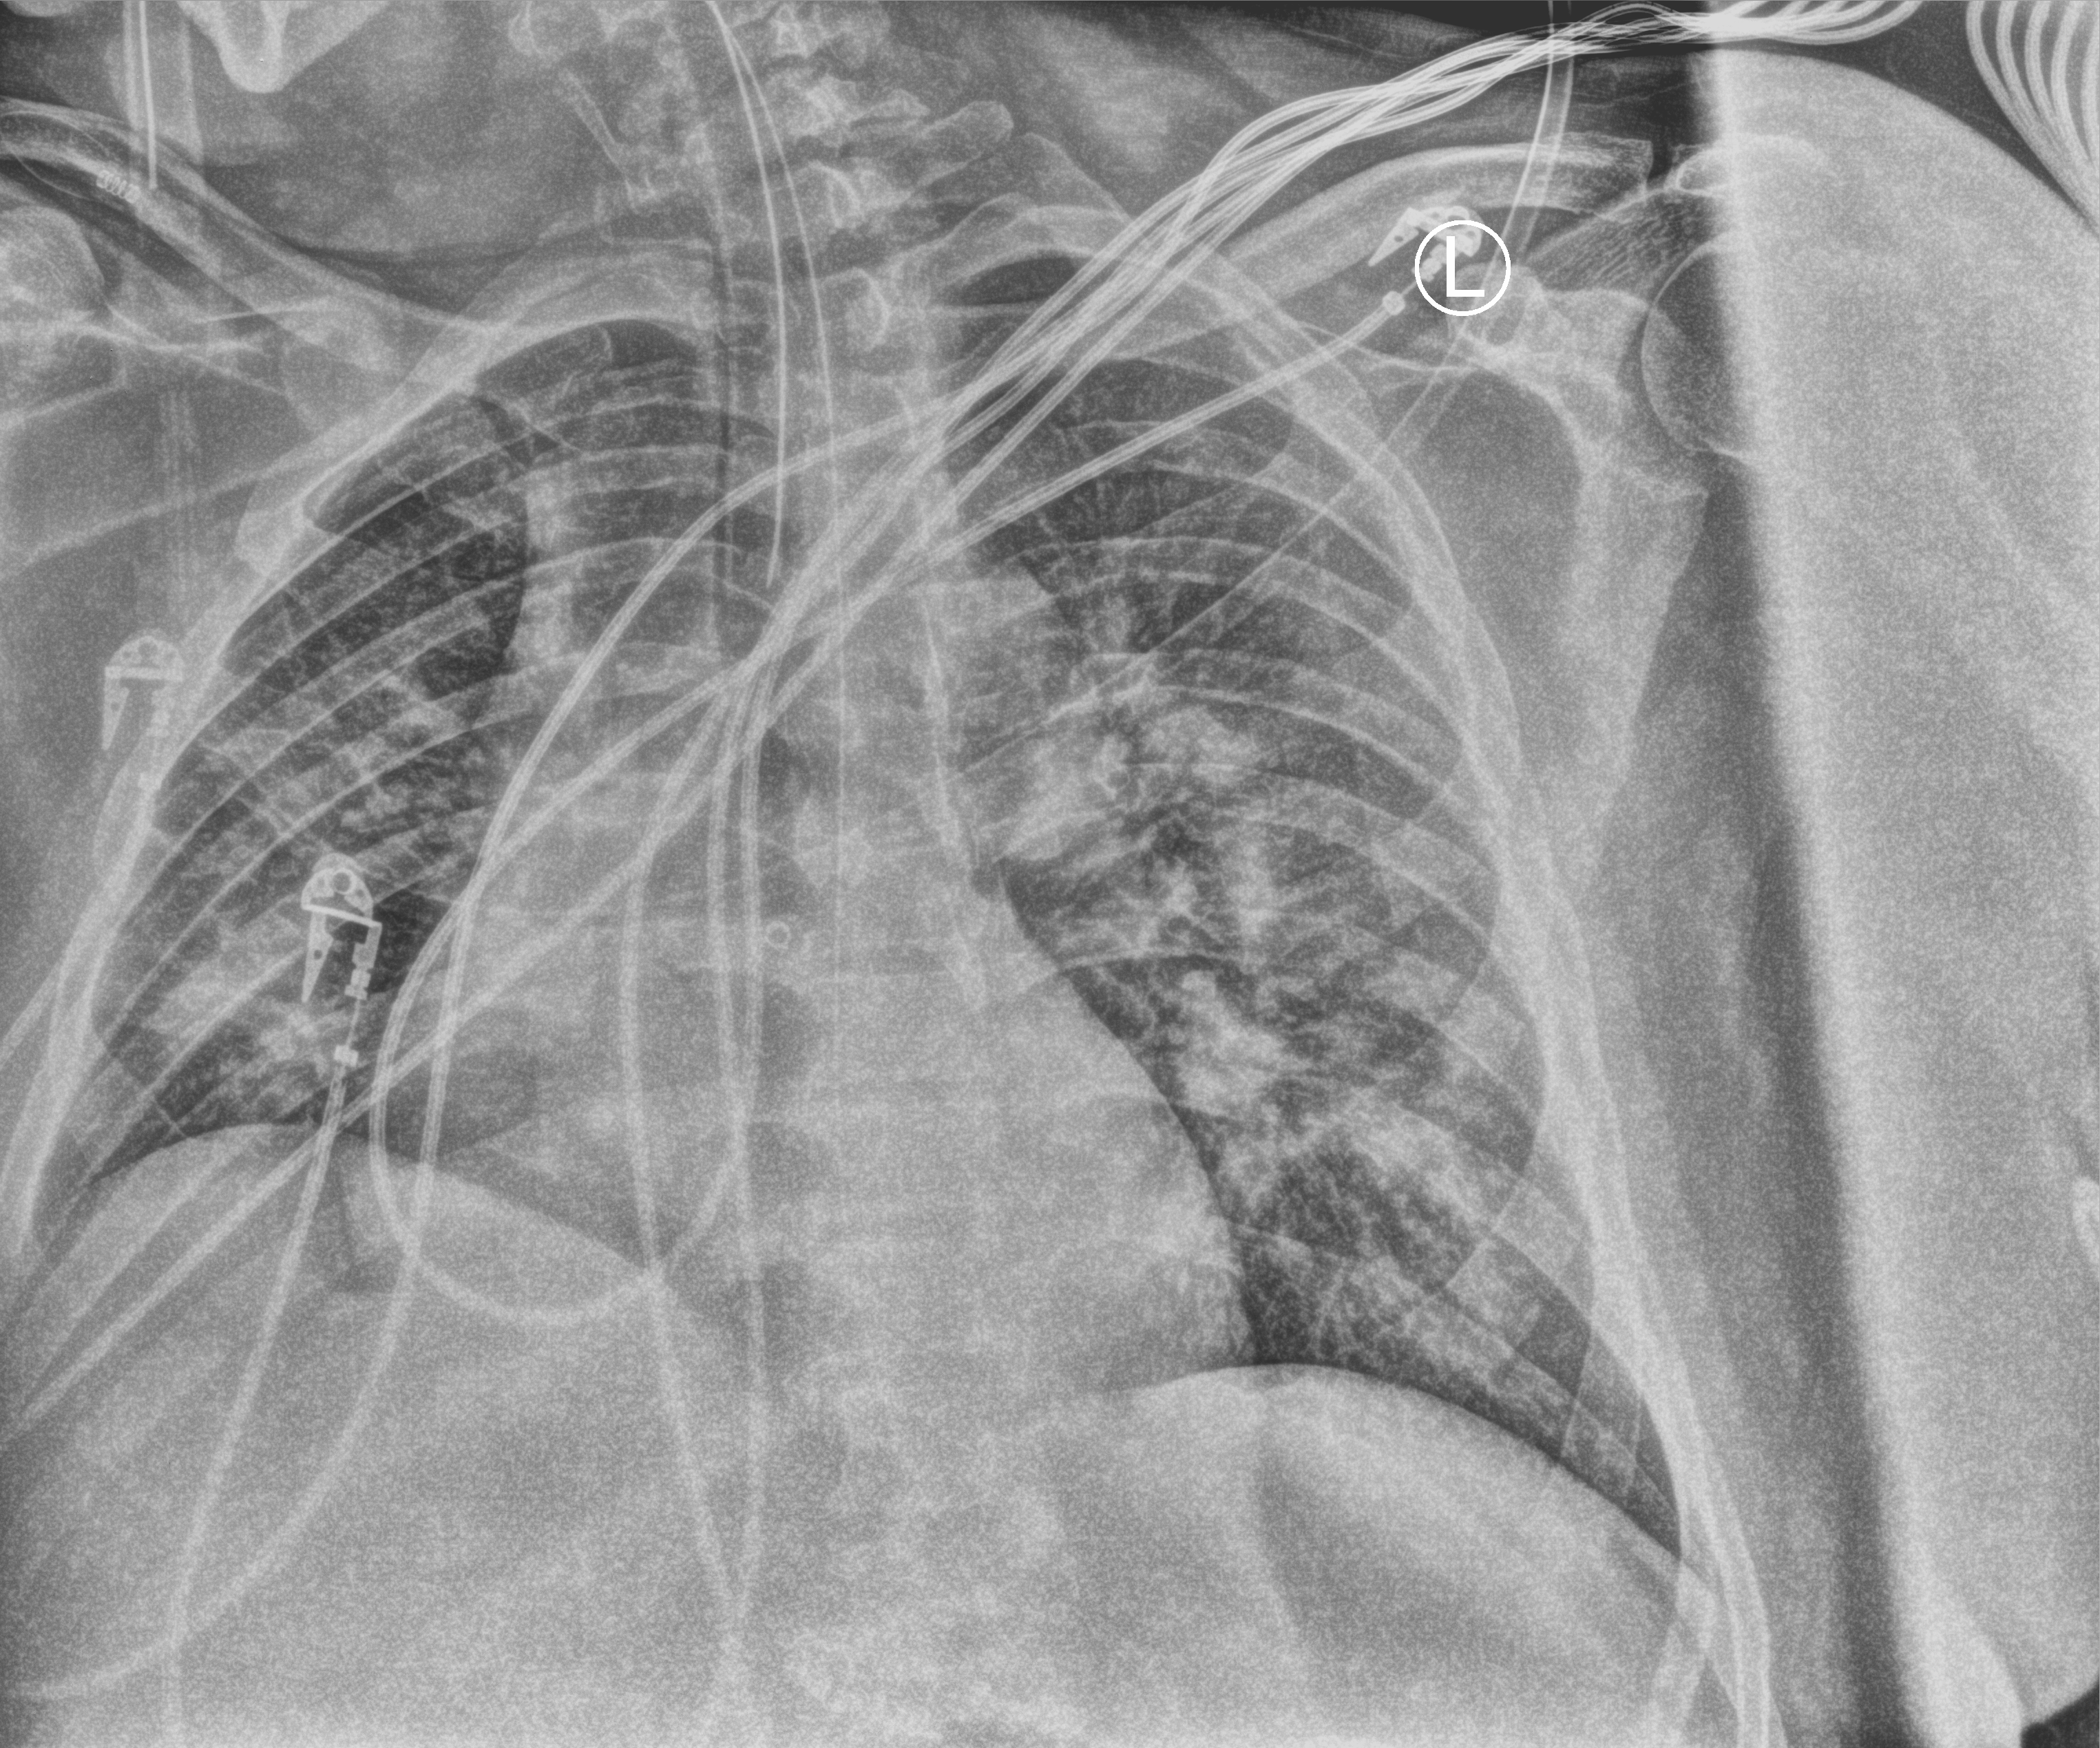
Portable chest radiograph; anteroposterior (AP) projection. Male patient hospitalised with COVID-19, age 60–74 years.
Hospital-stay facts (about this admission, not read from this image; timing relative to this image not recorded):
- other chronic lung disease (admission record): no